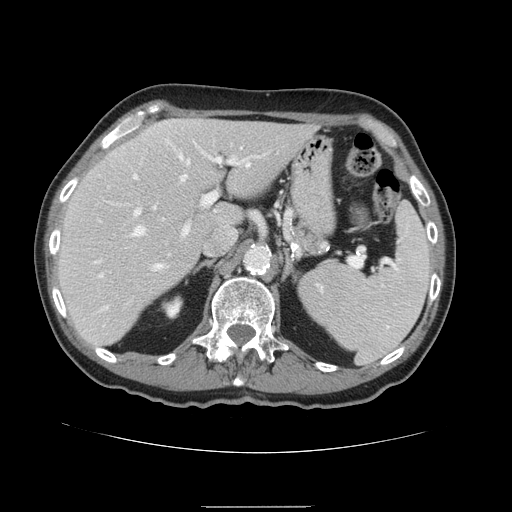
Contrast-enhanced abdominal CT, one axial slice. Slice 99 of 168 in the series (ordered by position). 120 kVp. Intravenous contrast given. Soft-tissue window (W 400 / L 40 HU). 2.5 mm slice thickness. 512 × 512 image matrix, field of view 386 × 386 mm. Male patient, age 74 years. Case-level facts recorded for this patient, not image findings: diagnosis: colorectal cancer liver metastases, imaged before liver resection; multiple liver metastases: no; largest metastasis: 14.5 cm; disease in both lobes: yes.
Structures marked on this image (outlined manually by an expert reader):
- hepatic veins: bounding box <134,155,250,268> (left, top, right, bottom; pixels)
- liver: <57,119,318,346>
- planned liver remnant (the part of the liver to remain after resection): <58,120,318,346>
- portal vein (with intrahepatic branches): <93,157,238,276>